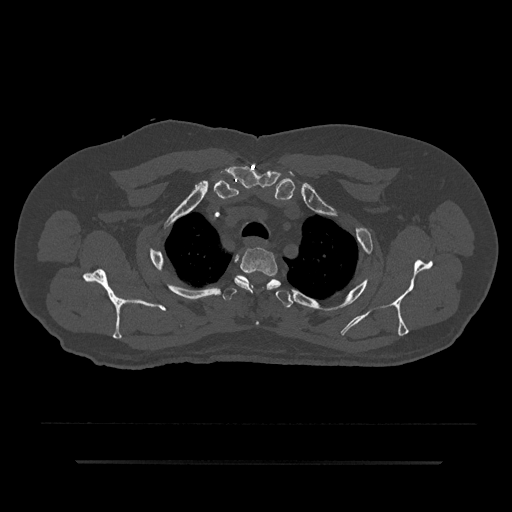
CT including the spine, one axial slice; position 683 of 797 along the scan axis; 120 kVp; bone window (W 1800 / L 400 HU); 0.5 mm slice thickness; 512 × 512 image matrix, field of view 464 × 464 mm. Male patient, age 59 years. Case-level facts recorded for this patient, not image findings: primary cancer: bile ducts.
Outlined on this slice (semi-automatic segmentation, software-assisted and operator-edited):
- T2 vertebra: bounding box (x1, y1, x2, y2) in pixels: (234, 247, 278, 325)
- T3 vertebra: (223, 275, 293, 308)